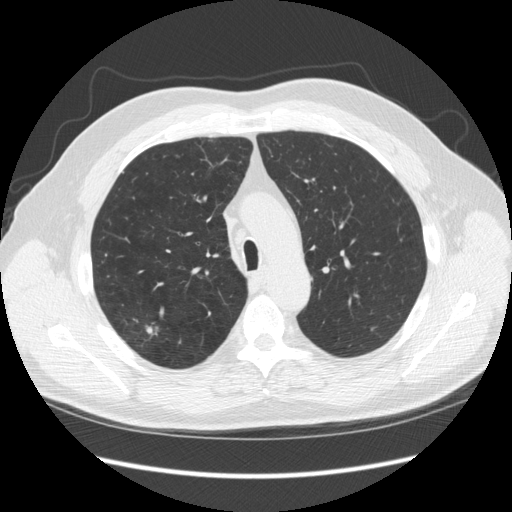
Low-dose screening chest CT, one axial slice. Slice 179 of 248 in the series (ordered by position). Reconstruction kernel STANDARD. Lung window (W 1500 / L -600 HU). 2.5 mm slice thickness. 512 × 512 image matrix.
Annotated regions visible in this slice (outlined manually by an expert reader):
- lesion 1 (tumor, upper lobe of right lung): box from (x=146, y=326) to (x=153, y=334) px